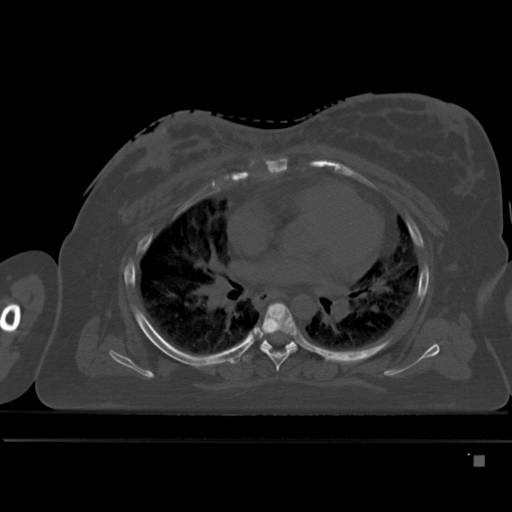
CT including the spine, one axial slice. Position 314 of 495 along the scan axis. Bone window (W 1800 / L 400 HU). 1.5 mm slice thickness. 512 × 512 image matrix, field of view 404 × 404 mm. Patient: female, 33 years. From the clinical record (not read from this slice): primary cancer: breast; vertebrae with lytic lesions (as recorded): T1.
Annotated regions visible in this slice (semi-automatic segmentation, software-assisted and operator-edited):
- T5 vertebra: bounding box [x1, y1, x2, y2] px = [260, 302, 298, 371]
- T6 vertebra: [244, 336, 300, 361]